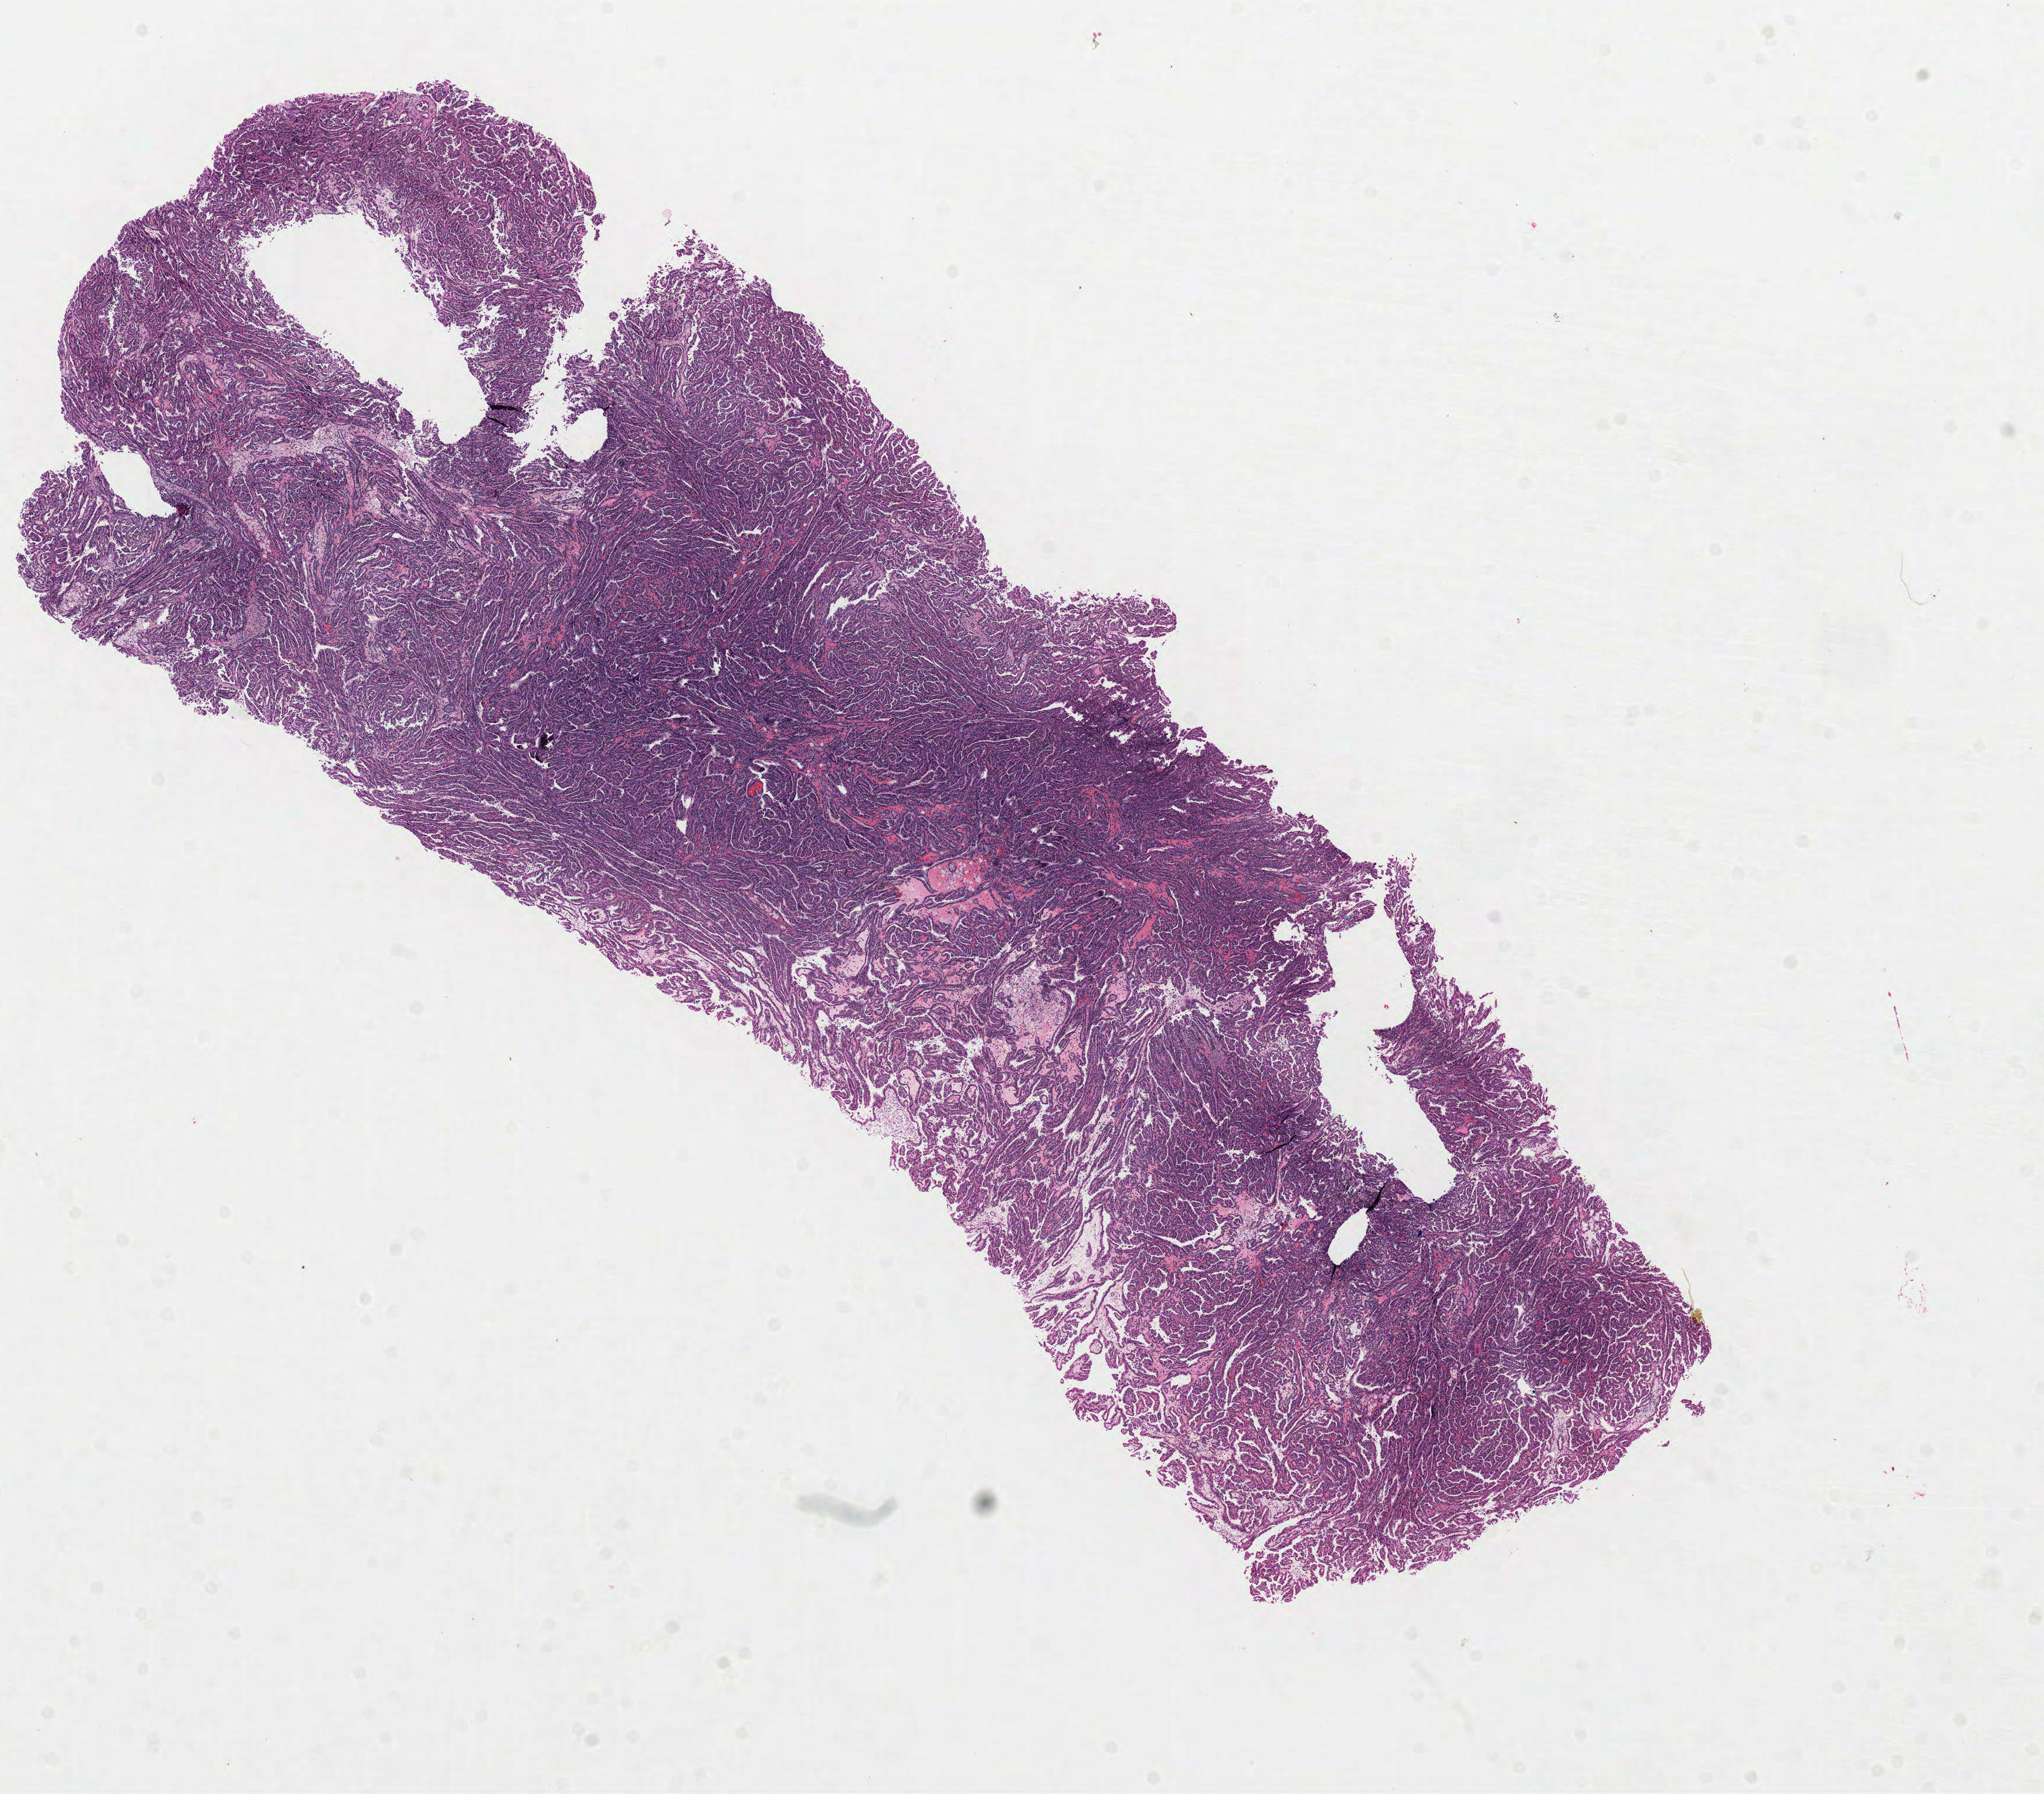
Whole-slide histology image, H&E, whole scanned area (about 14.1 x 12.3 mm) shown as a low-resolution overview. Formalin-fixed paraffin-embedded (FFPE) diagnostic section. Kidney, primary tumour sample. Male, age 41 years at initial diagnosis.
Laterality: left. Diagnosis: Papillary adenocarcinoma, NOS.